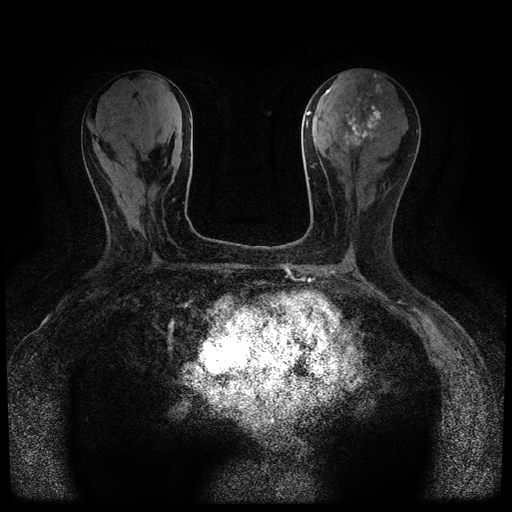
Breast MRI (dynamic contrast-enhanced, multi-phase), one axial slice; position 33 of 116 along the scan axis; dynamic contrast-enhanced series, time point 2 of 5 at this slice position (early post-contrast); 1.5 T; TE 2.7 ms, TR 5.4 ms; 512 × 512 image matrix. Female patient, age 80 years.
Annotated regions visible in this slice (semi-automatically segmented with operator editing):
- breast lesion (labelled 'tumour' in the annotation; benign lesions carry a separate 'benign' label): box from (x=344, y=80) to (x=381, y=148) px